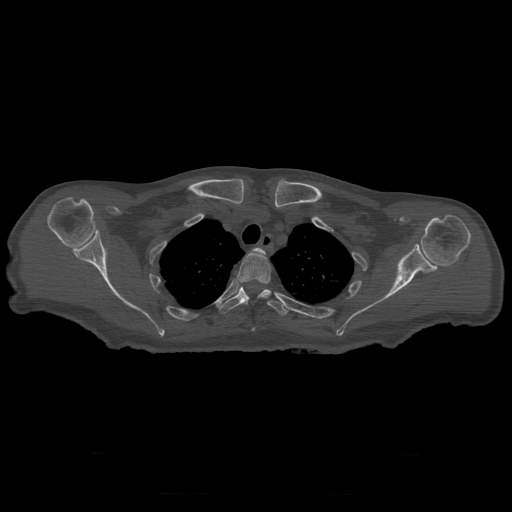
CT including the spine, one axial slice. Reconstruction kernel STANDARD. 120 kVp. Bone window (W 1800 / L 400 HU). 1.25 mm slice thickness. 512 × 512 image matrix, field of view 510 × 510 mm. Patient age 73 years. Case-level facts recorded for this patient, not image findings: primary cancer: prostate.
Annotated regions visible in this slice (semi-automatic segmentation, software-assisted and operator-edited):
- T2 vertebra: bounding box [x1, y1, x2, y2] px = [254, 248, 266, 255]
- T3 vertebra: [237, 250, 271, 294]
- T4 vertebra: [219, 287, 288, 316]